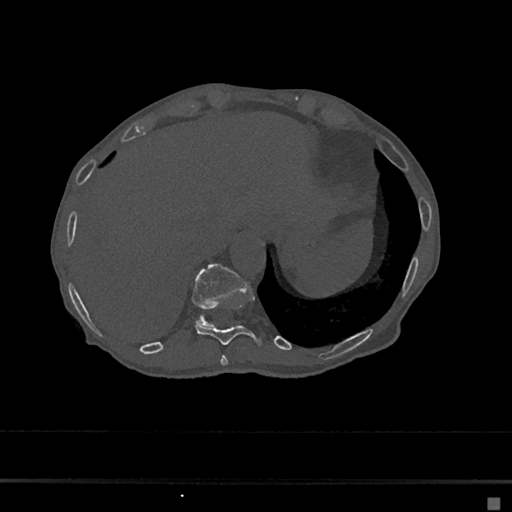
CT including the spine, one axial slice. Position 211 of 797 along the scan axis. Reconstruction kernel Br40s/3. Bone window (W 1800 / L 400 HU). 0.5 mm slice thickness. 512 × 512 image matrix. Patient: female, 68 years. Case-level facts recorded for this patient, not image findings: primary cancer: renal.
Structures marked on this image (semi-automatically segmented with operator editing):
- T10 vertebra: box from (x=195, y=305) to (x=263, y=347) px
- T11 vertebra: (x=192, y=263)–(x=248, y=326)
- T9 vertebra: (x=220, y=355)–(x=228, y=366)